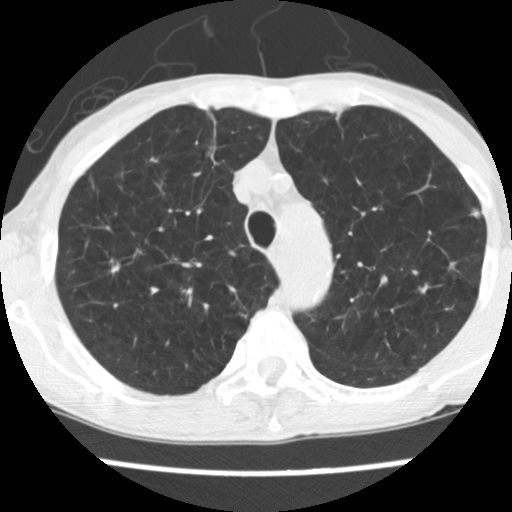
Chest CT (low-dose screening protocol), one axial image, baseline annual screen, lung window (W 1500 / L -600 HU), 2.5 mm slice thickness, 120 kVp, slice 40 of 160 in the series. Female, age 70 years at enrolment.
Expert-annotated lung lesion, box from (x=93, y=244) to (x=142, y=288) px. No non-calcified nodule or mass ≥4 mm was recorded by the screening reader at this exam. Lung cancer was diagnosed 226 days after this screen: large cell neuroendocrine carcinoma, right upper lobe, stage IA (AJCC 6th edition), 30 mm at pathology.